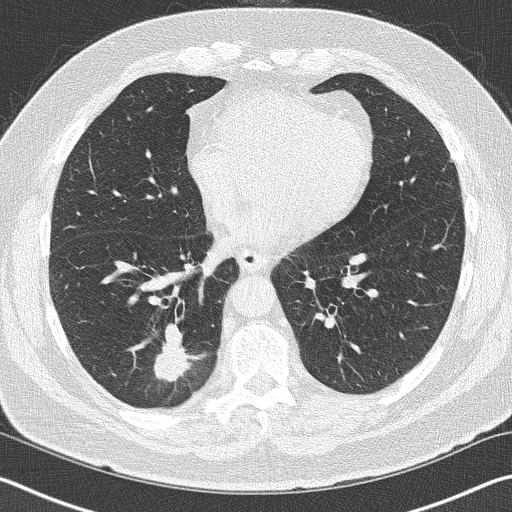
Chest CT (low-dose screening protocol), one axial image; baseline screening round; lung window (W 1500 / L -600 HU); 2 mm slice thickness; slice 98 of 141 in the series. Male participant, aged 70 years at enrolment. Current smoker at enrolment.
- Expert-annotated lung lesion, bounding box [x1, y1, x2, y2] px = [140, 329, 213, 401].
- Screening reader's record for this exam (one nodule recorded; not confirmed to be the boxed lesion): non-calcified nodule or mass ≥4 mm, right lower lobe, 28 × 23 mm, spiculated (stellate) margins, soft tissue attenuation.
- Official screen result: positive, change unspecified: nodule(s) >= 4 mm or enlarging nodule(s), mass(es), or other non-specific abnormalities suspicious for lung cancer.
- Later outcome: lung cancer diagnosed 62 days after this screen — squamous cell carcinoma, NOS, right lower lobe, poorly differentiated (G3), stage IB (AJCC 6th edition), 24 mm at pathology.